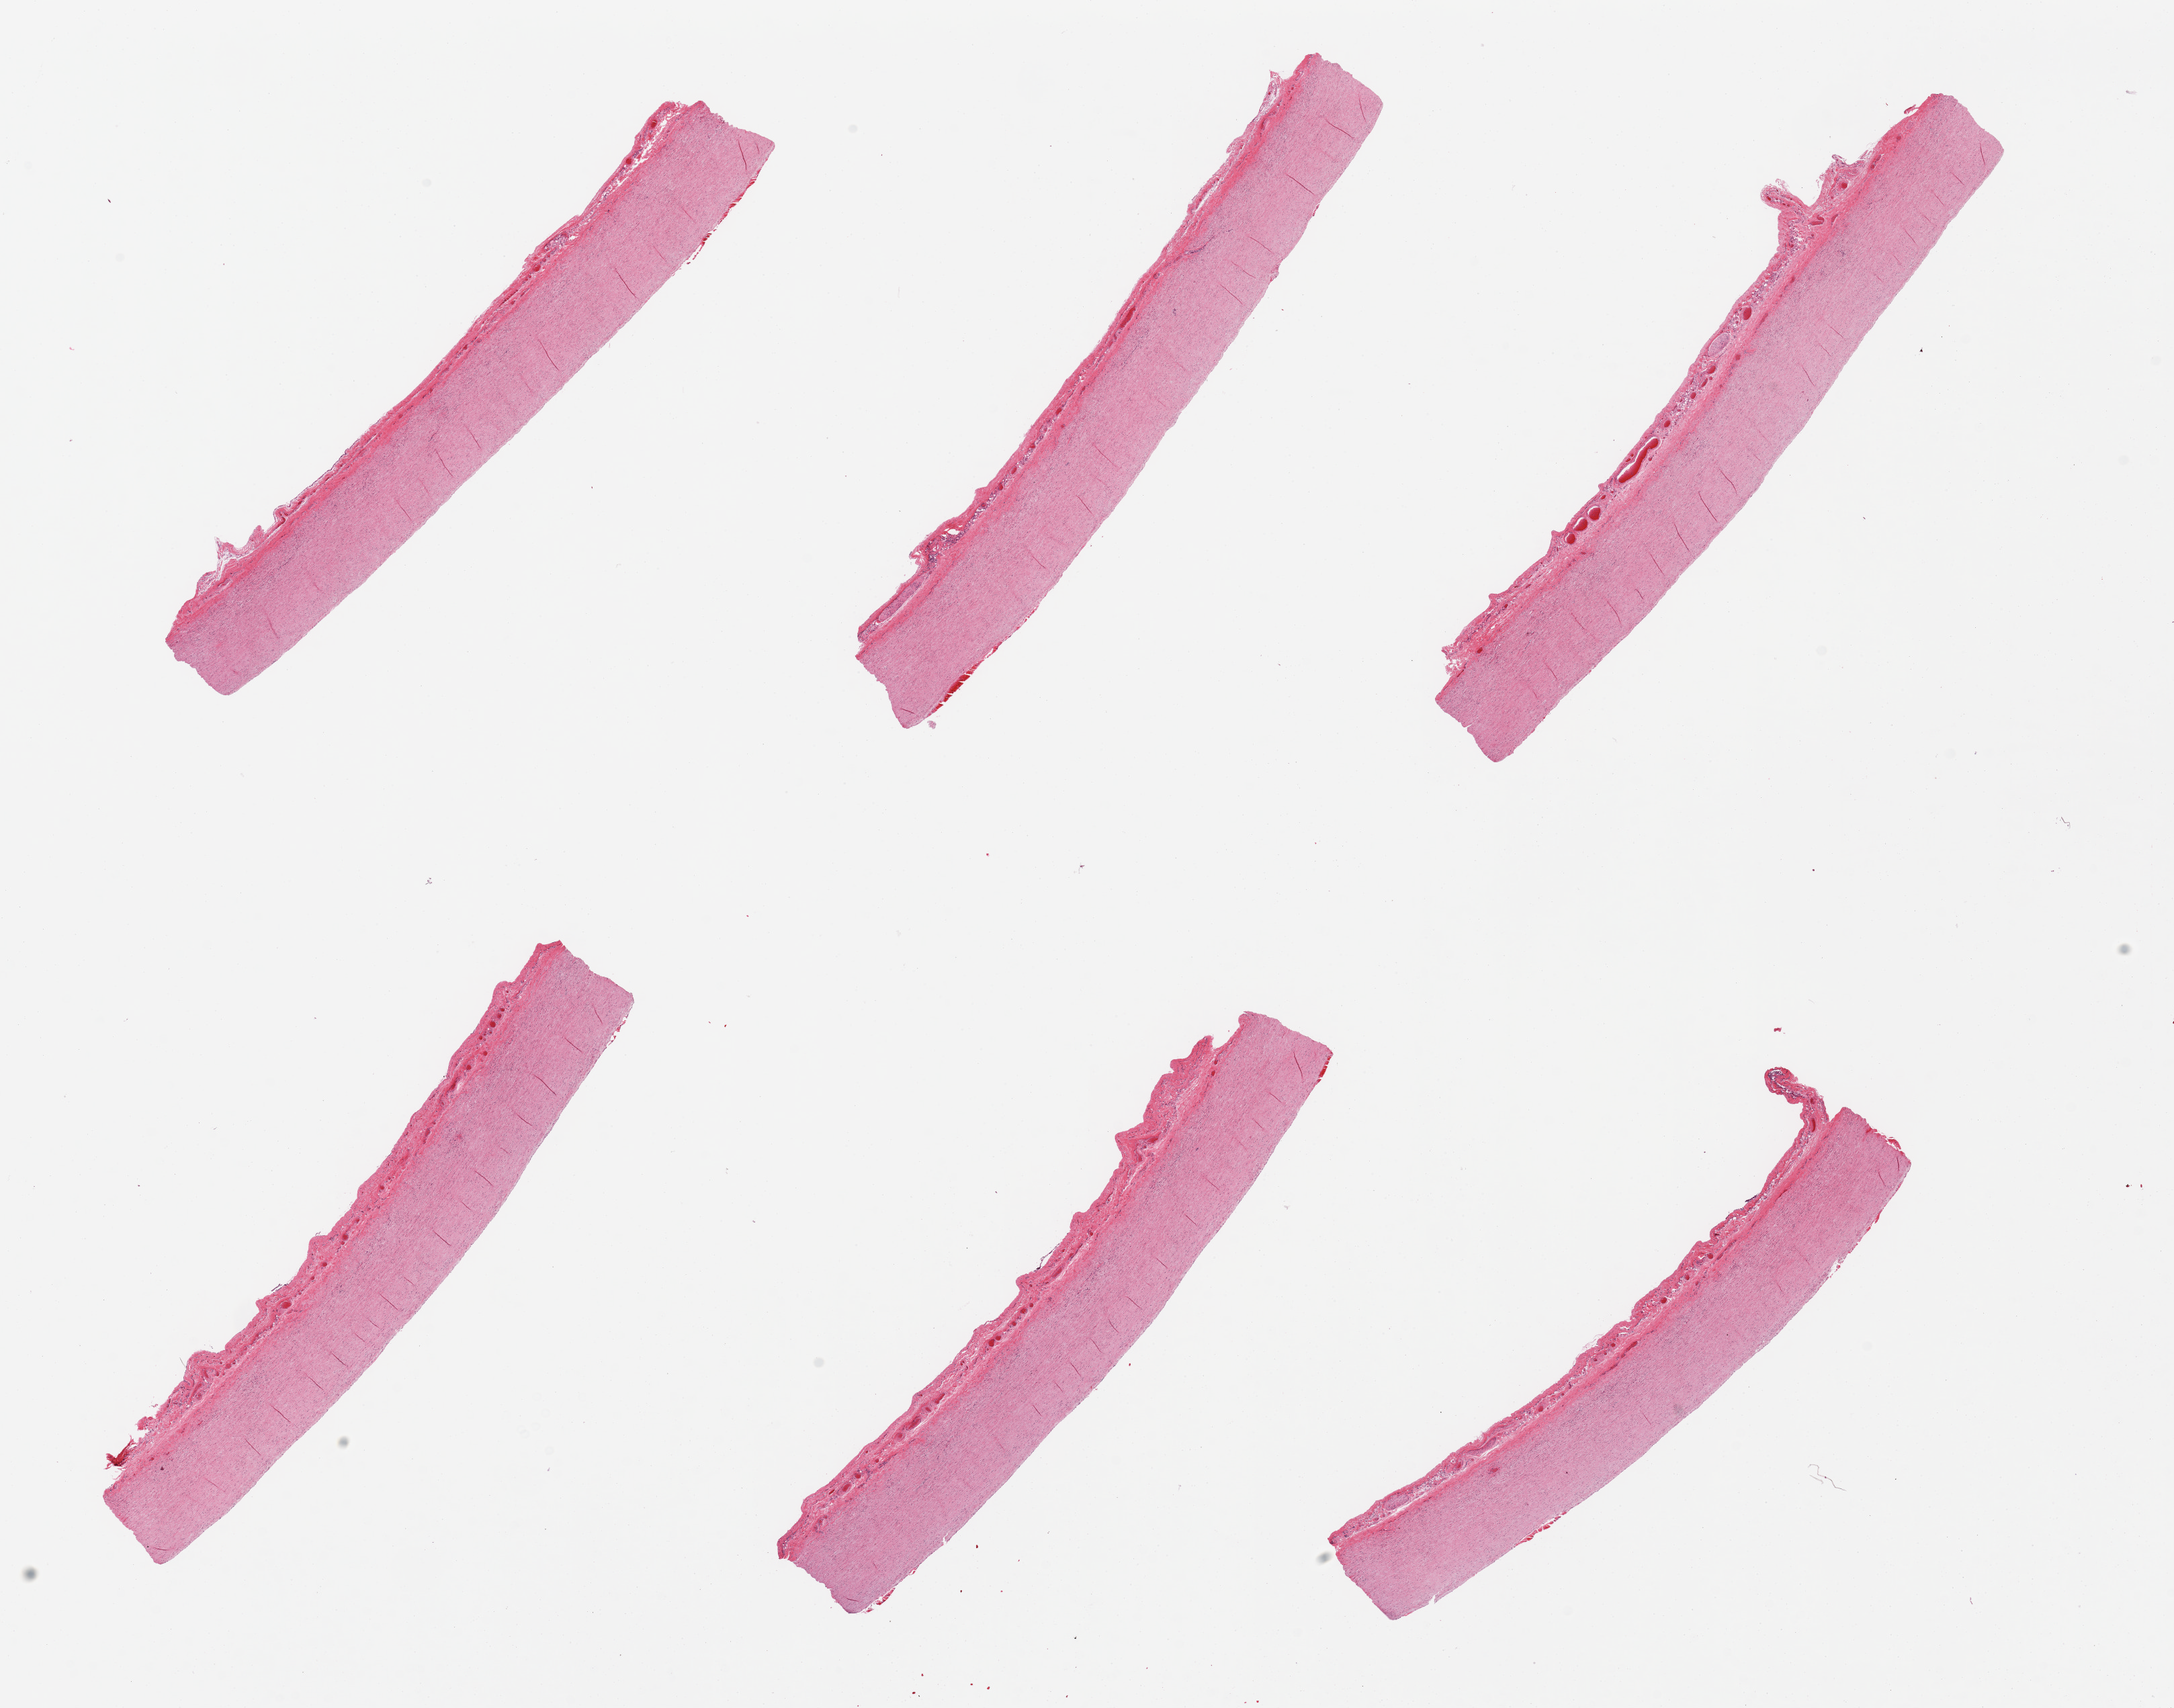
Haematoxylin and eosin whole-slide image — a low-resolution overview of the entire scanned area, about 25.6 x 20.1 mm (slide scanned at 20x), PAXgene-fixed, paraffin-embedded tissue, section of aorta (target tissue), donor tissue sample. Male donor.
- reviewer comment on this tissue sample: 6 pieces, minimal atherosis